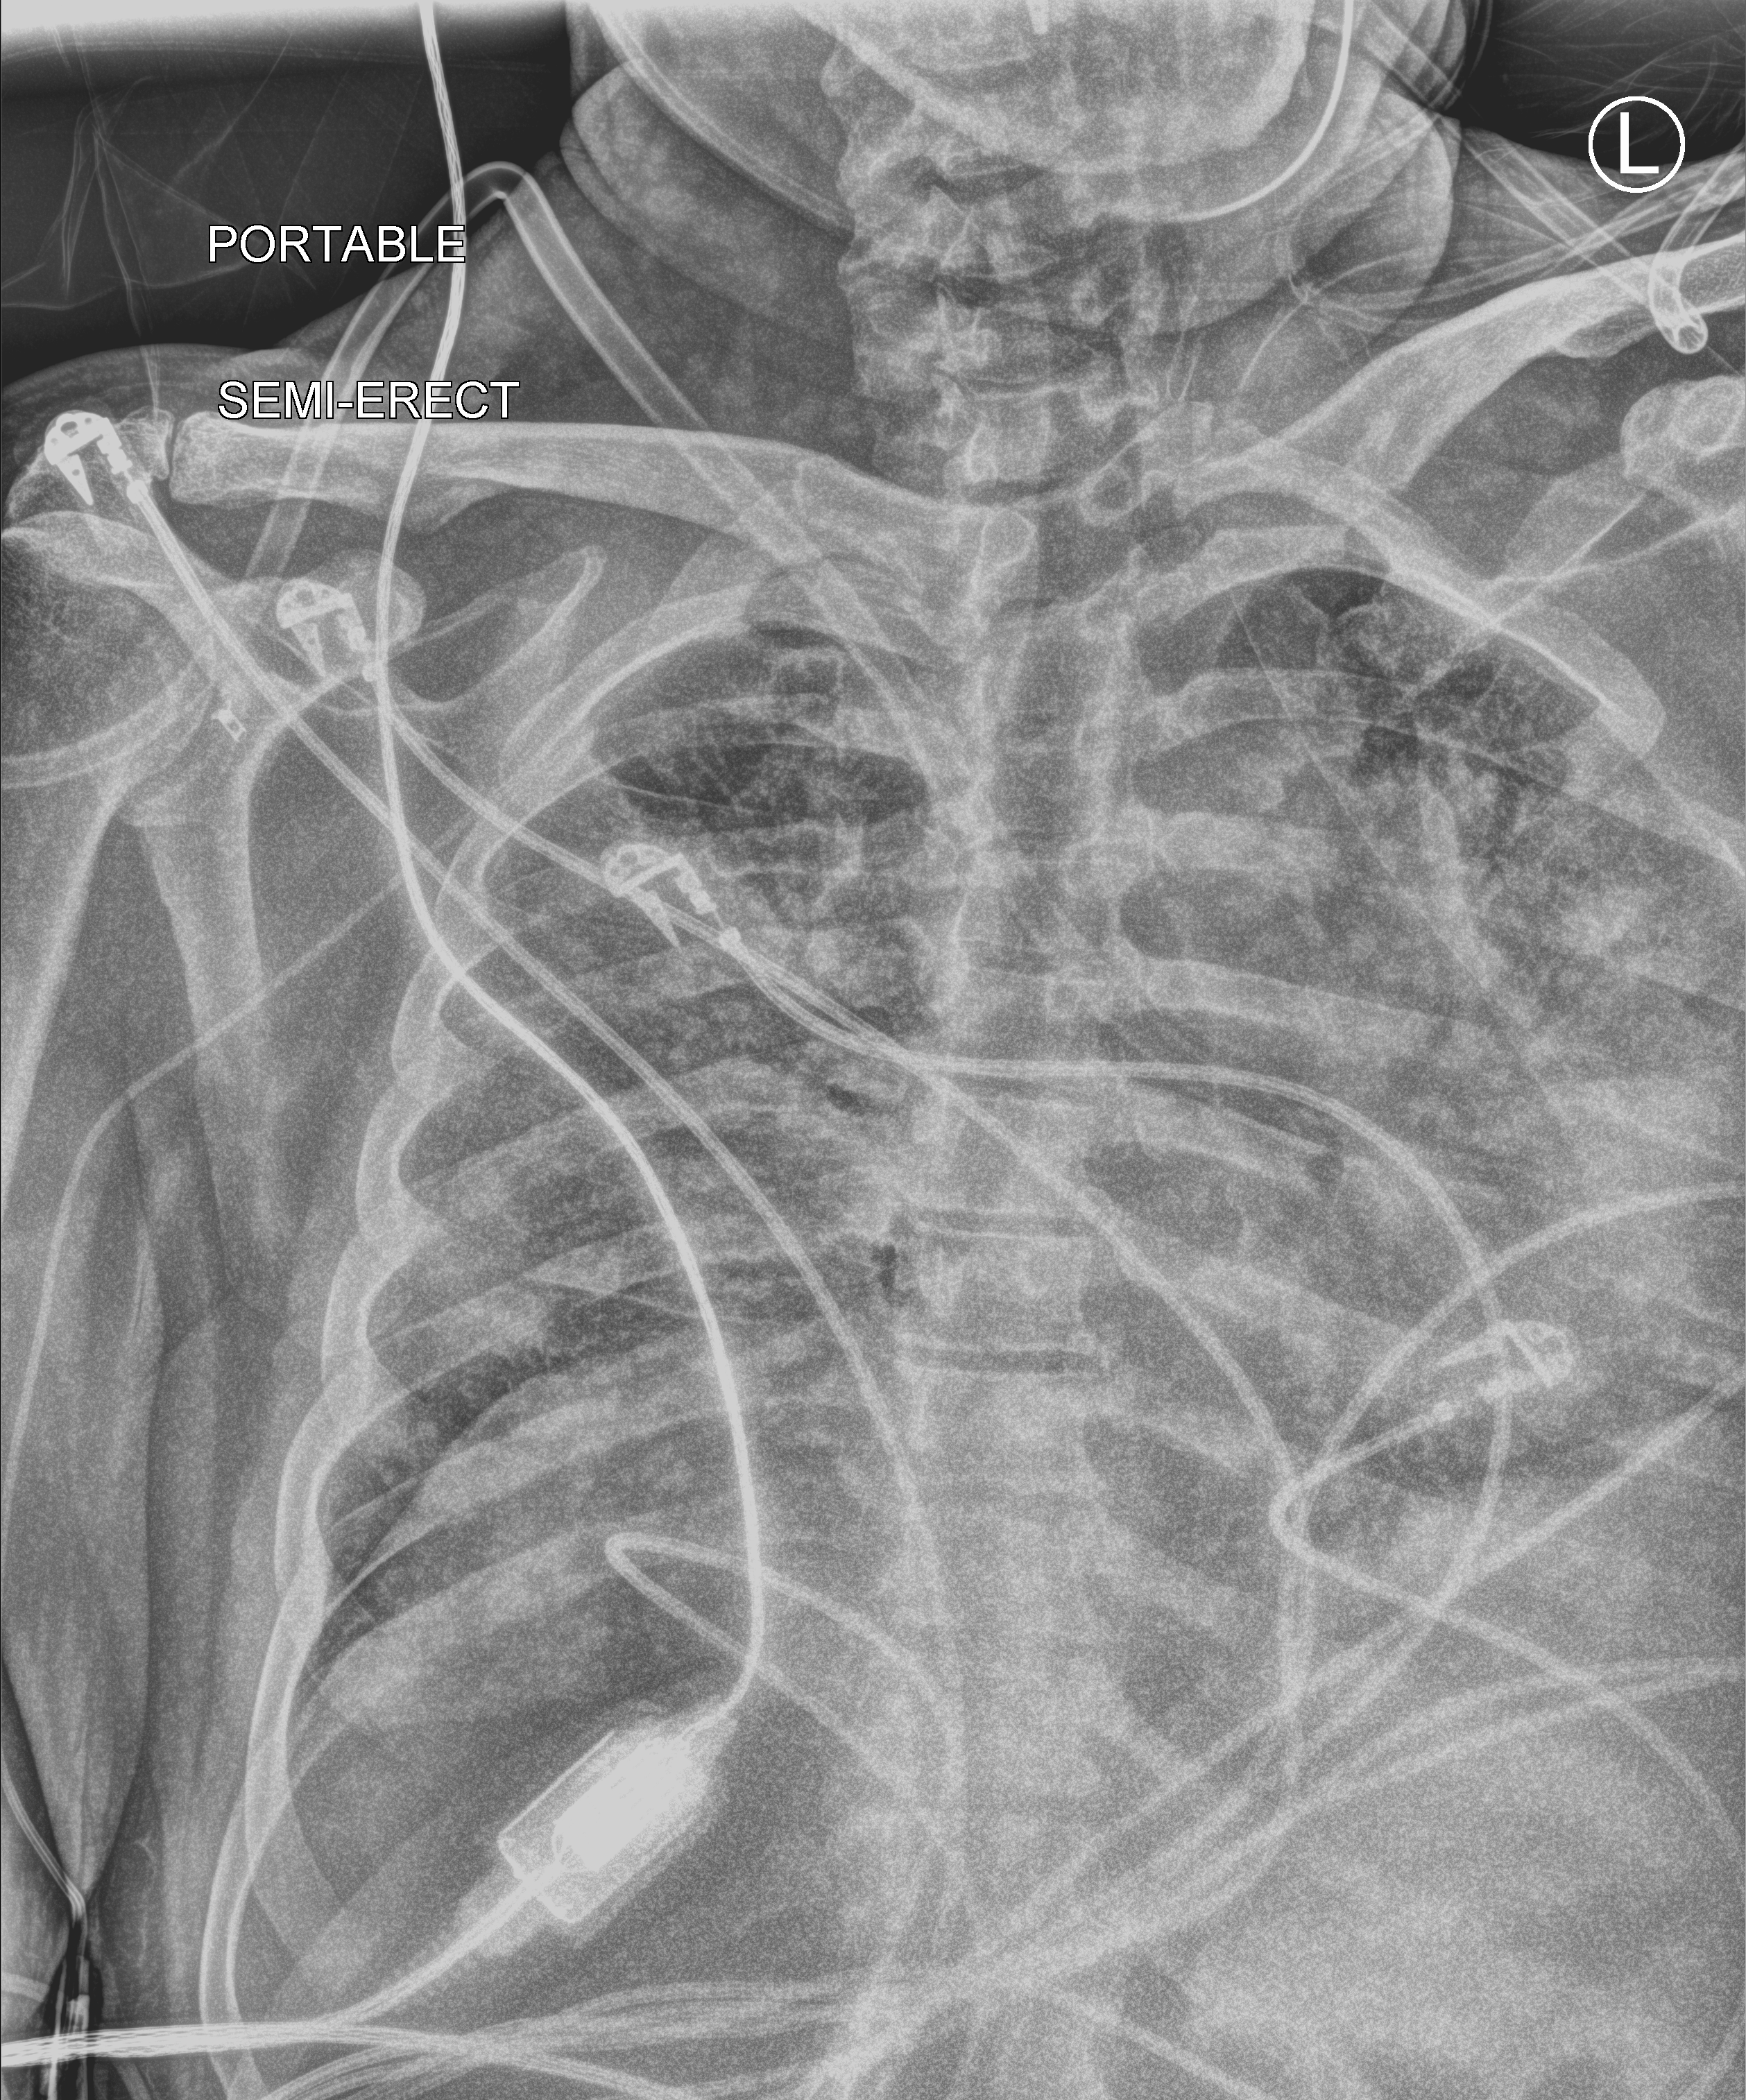
Bedside chest radiograph (computed radiography), anteroposterior (AP) projection. Male patient hospitalised with COVID-19, age 18–59 years.
Hospital-stay facts (about this admission, not read from this image; timing relative to this image not recorded):
- hypertension (admission record): no